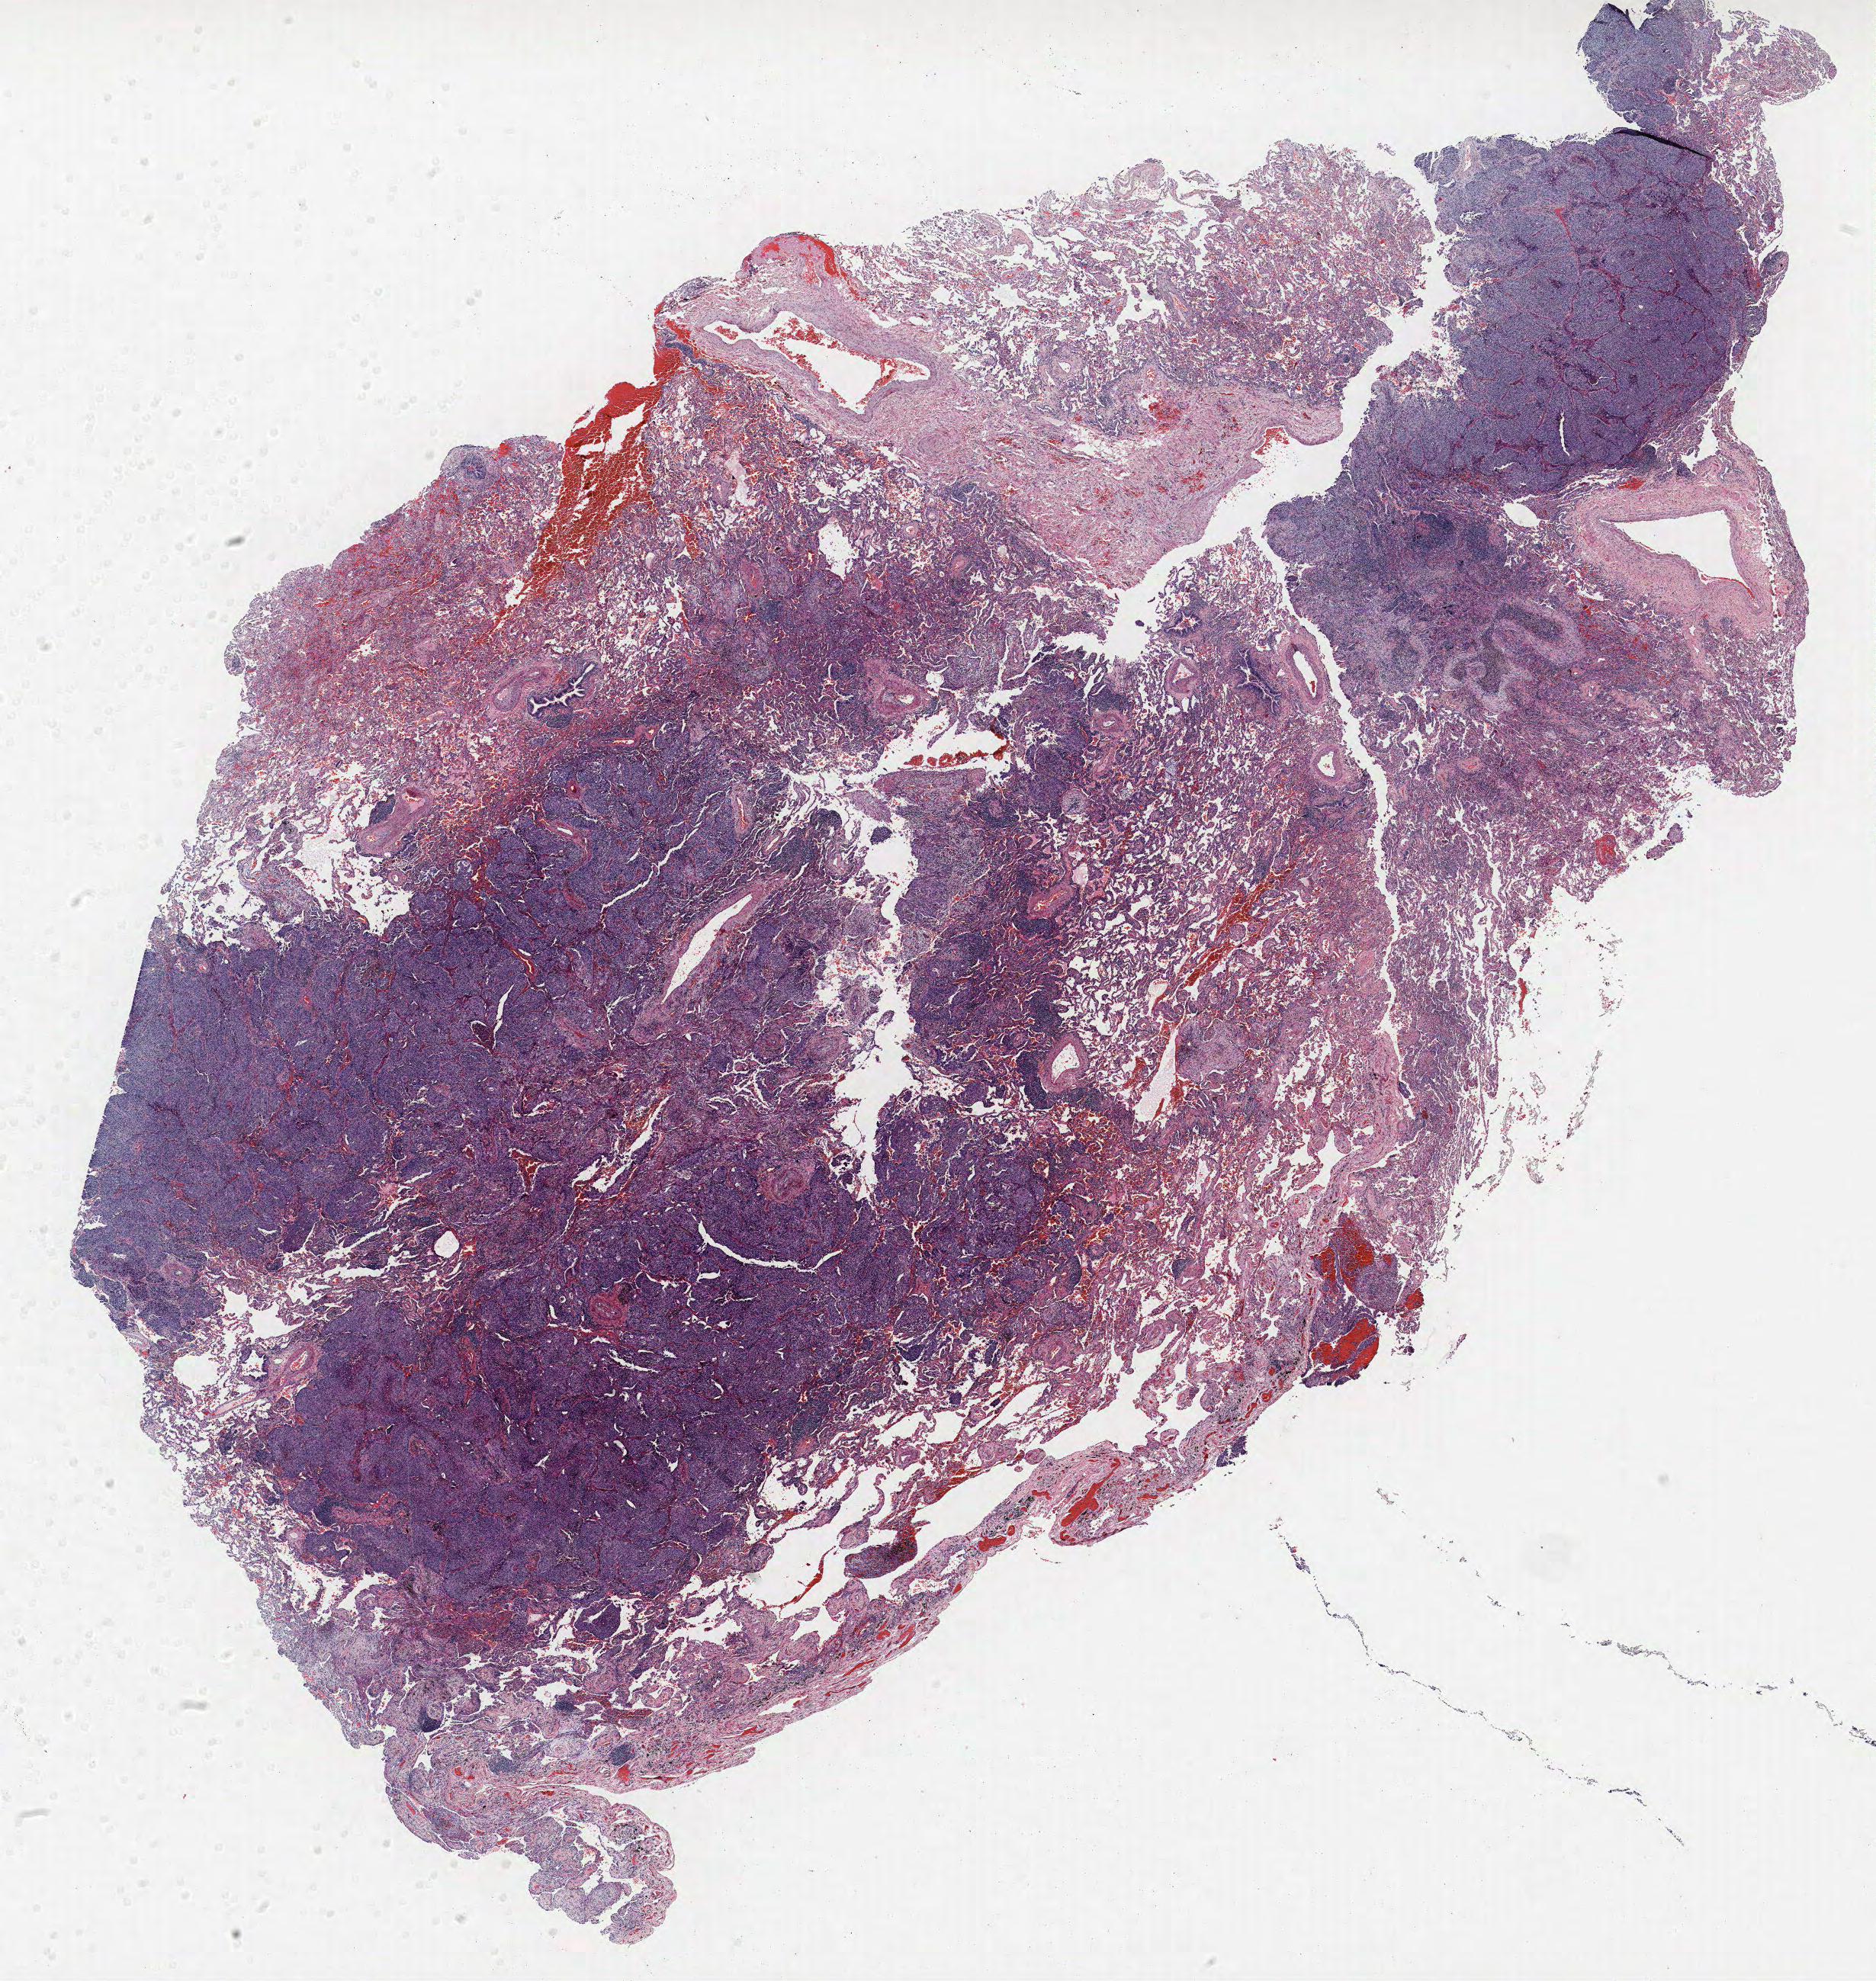
Hematoxylin and eosin (H&E) stained whole-slide image — a low-resolution overview of the entire scanned area, about 19.7 x 20.8 mm; FFPE section; lung. Male, age 59 at enrolment. Former smoker at enrolment. Grade: moderately differentiated (G2).
Participant's lung-cancer diagnosis: Squamous cell carcinoma, NOS. Stage (AJCC 6th edition): IA. ICD-O-3 topography: lower lobe of lung (C34.3). Tumour size (pathology): 15 mm. Primary tumour location (clinical record): right lower lobe.